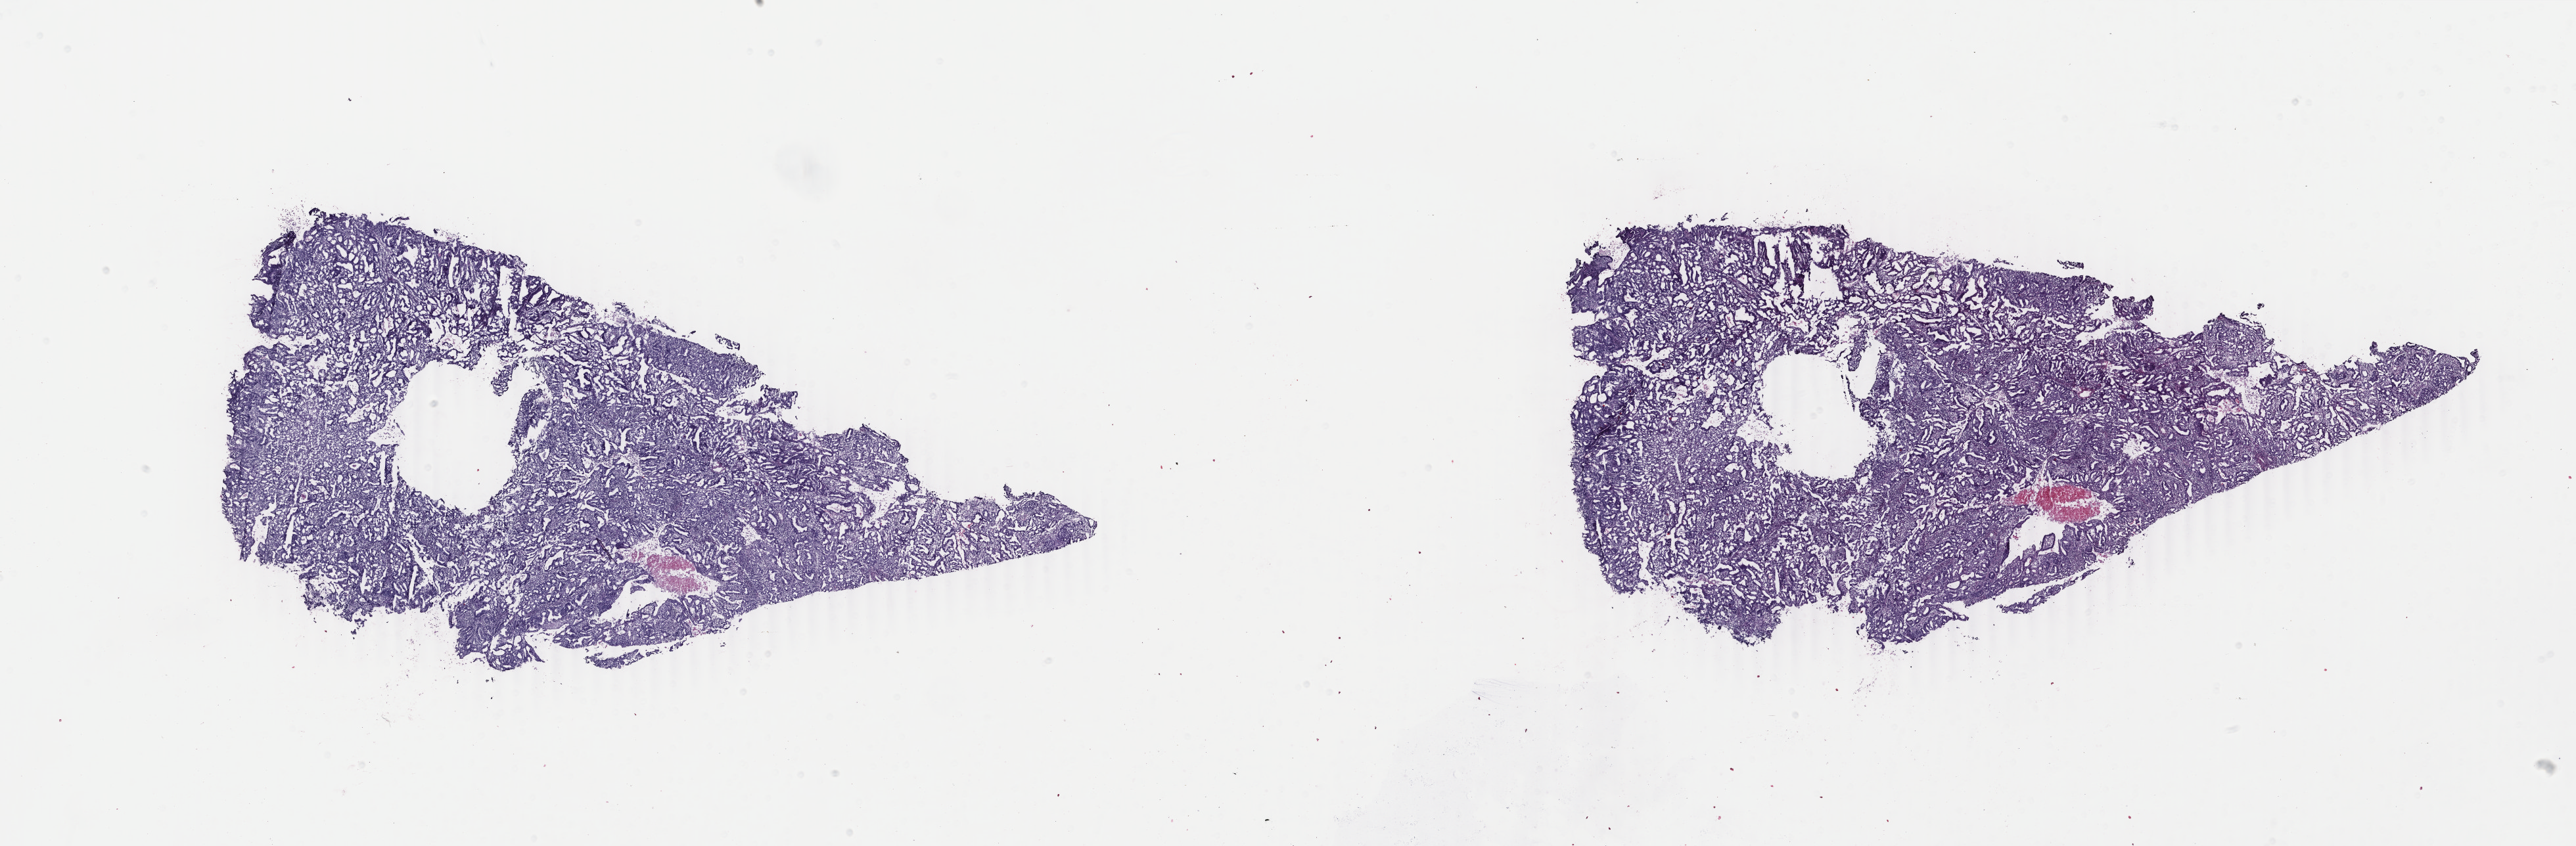
H&E whole-slide image, whole scanned area (about 31.2 x 10.2 mm) shown as a low-resolution overview. Frozen section. Uterus, primary tumour sample. Patient: female, age at initial diagnosis 60 years. Histologic grade: G3 (poorly differentiated). Pathologist review of this section (percent, as recorded): tumour cells 60%, tumour nuclei 70%, normal cells 0%, stromal cells 30%, necrosis 10%. Infiltration values recorded for this section: lymphocyte infiltration 20%, monocyte infiltration 0%, neutrophil infiltration 10%.
- FIGO stage: IIIC1
- lymph nodes positive (case pathology): 1 of 19 examined
- histologic diagnosis: Endometrioid adenocarcinoma, NOS (endometrium)